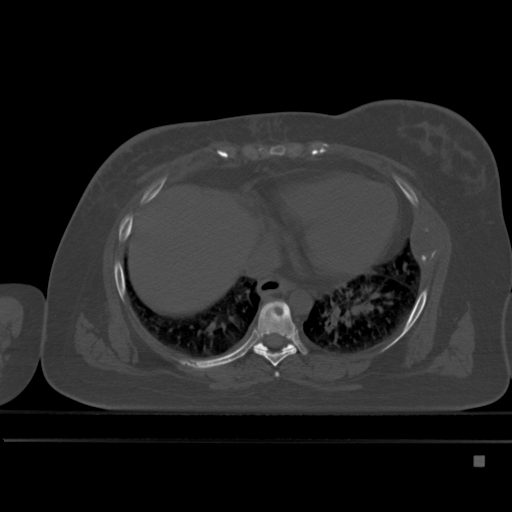
CT including the spine, one axial slice. Position 287 of 495 along the scan axis. Bone window (W 1800 / L 400 HU). 1.5 mm slice thickness. 512 × 512 image matrix, field of view 404 × 404 mm. Female patient, age 33 years. From the clinical record (not read from this slice): primary cancer: breast; vertebrae with lytic lesions (as recorded): T1.
Structures marked on this image (semi-automatically segmented with operator editing):
- T6 vertebra: bounding box <275,372,279,377> (left, top, right, bottom; pixels)
- T7 vertebra: <253,301,297,366>
- T8 vertebra: <250,339,296,351>